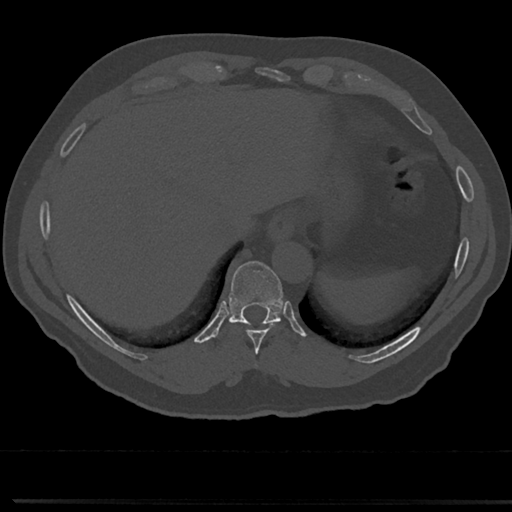
CT including the spine, one axial slice. Reconstruction kernel Br40s/3. 120 kVp. Bone window (W 1800 / L 400 HU). 0.5 mm slice thickness. 512 × 512 image matrix, field of view 355 × 355 mm. Patient: male, 61 years. From the clinical record (not read from this slice): primary cancer: prostate.
Outlined on this slice (semi-automatically segmented with operator editing):
- T10 vertebra: bounding box <231,315,279,322> (left, top, right, bottom; pixels)
- T8 vertebra: <254,322,276,371>
- T9 vertebra: <214,262,301,349>